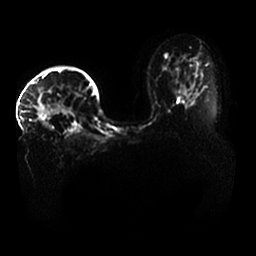
Breast MRI, one axial slice; slice 24 of 33 in the series (ordered by position); diffusion-weighted series; image 2 of 4 stored at this slice position (different b-values; order by instance number); 1.5 T; 256 × 256 image matrix, field of view 400 × 400 mm. Female patient.
Outlined on this slice (manually delineated by an expert):
- tumour on diffusion-weighted imaging: bounding box <34,104,51,130> (left, top, right, bottom; pixels)